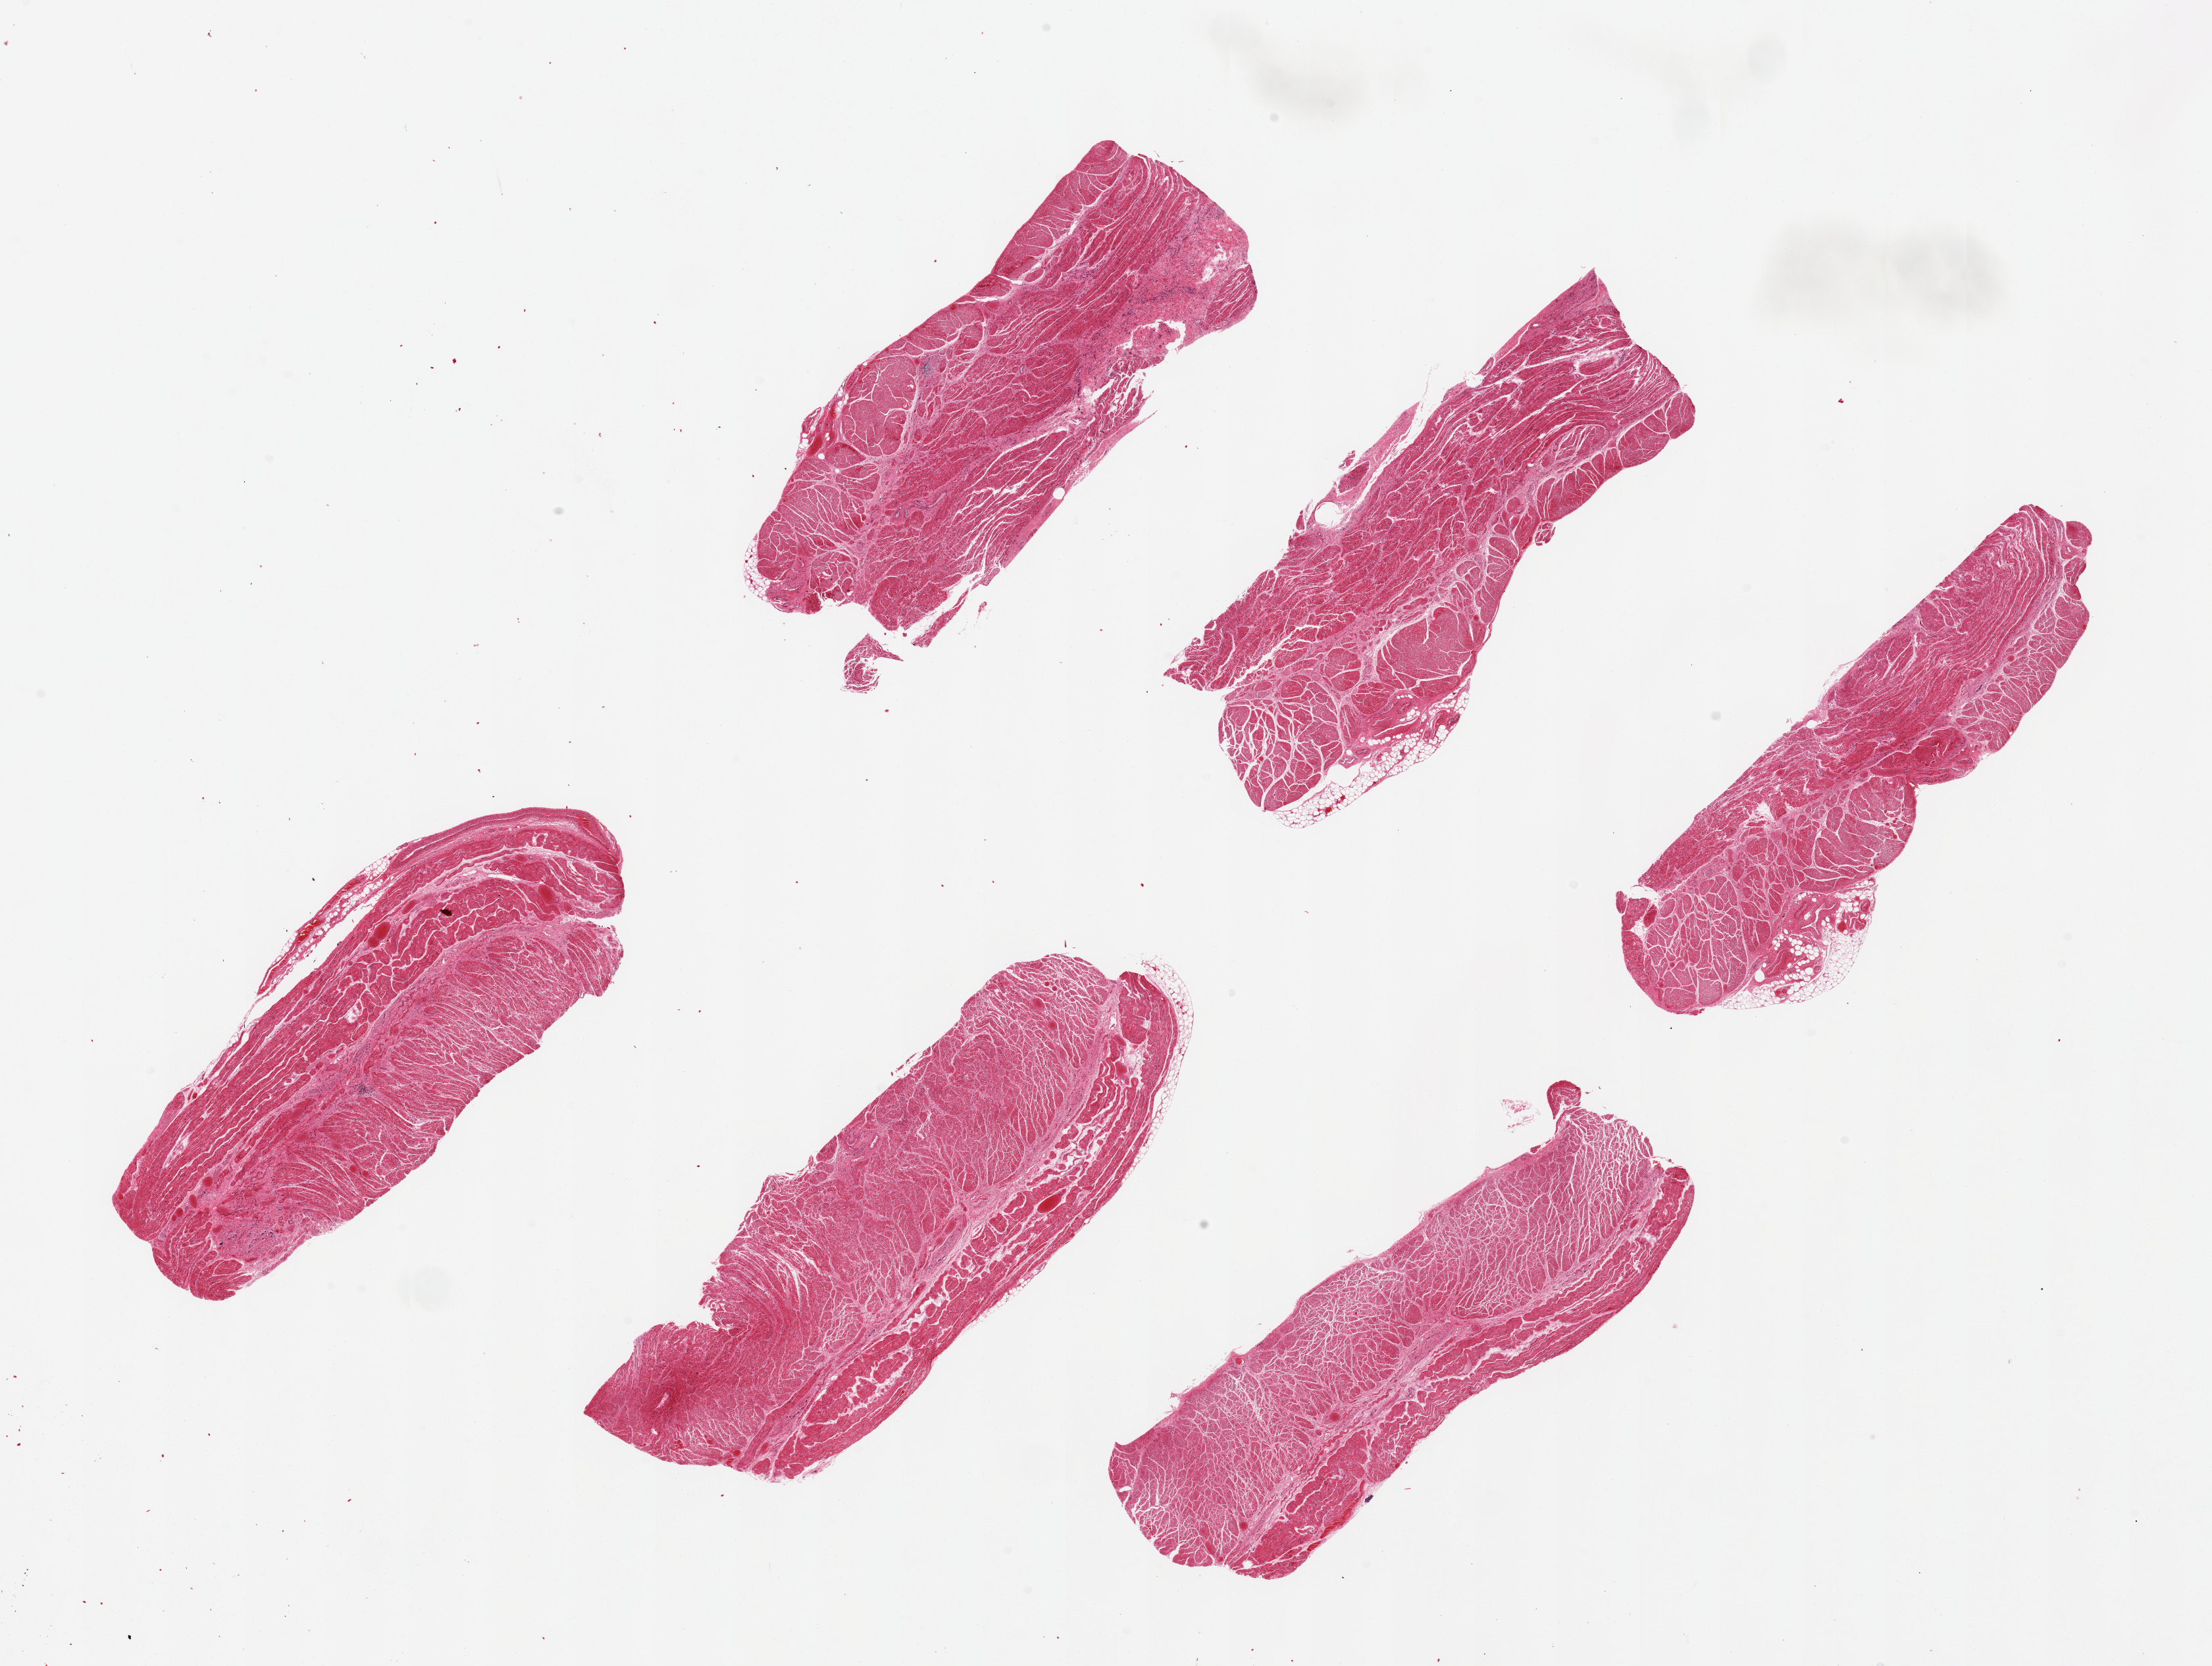
Whole-slide image, H&E stain — whole scanned area (about 26.6 x 20.0 mm, acquisition: 20x scan) shown as a low-resolution overview, PAXgene-fixed, paraffin-embedded tissue, target tissue: esophageal muscle, donor tissue sample. Donor sex: male.
Review note (as recorded): 6 pieces ~7x2.5mm.